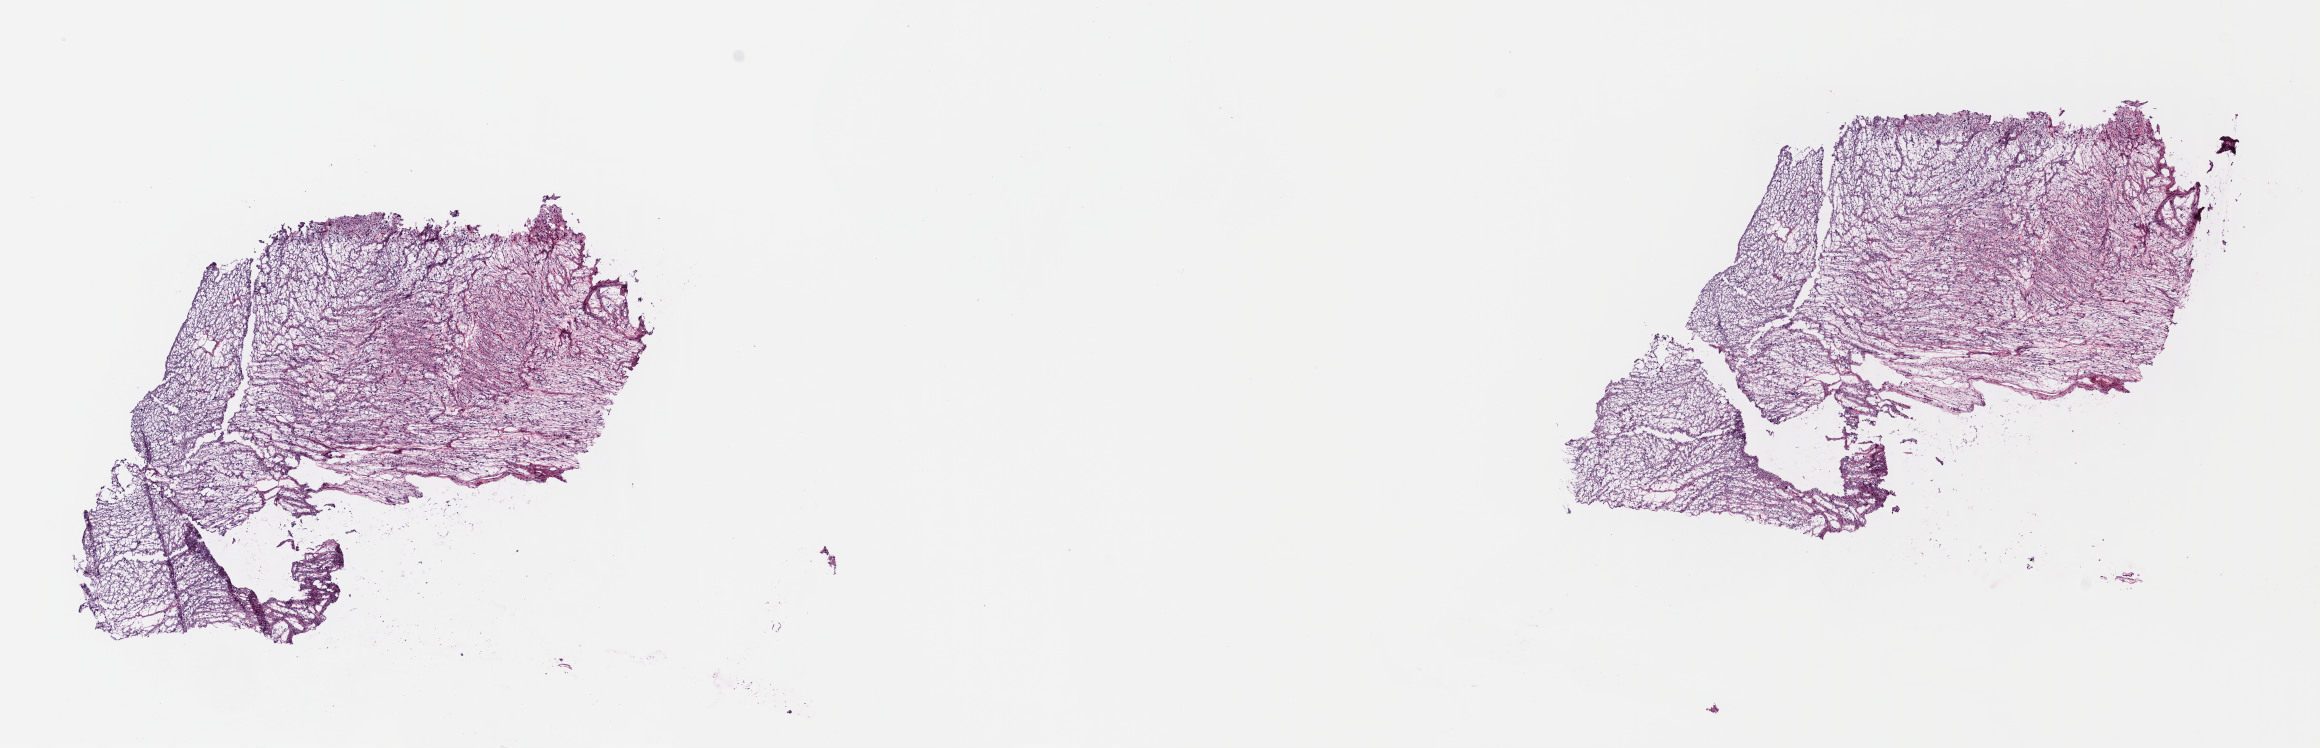
Whole-slide histology image, H&E-stained, whole scanned area (about 18.2 x 5.9 mm) shown as a low-resolution overview; frozen section from the top of the tissue portion; primary tumour sample from the connective, subcutaneous and other soft tissues. Male patient; age at initial diagnosis 59 years. Slide review estimates, as recorded: tumour cells 75%, tumour nuclei 75%, normal cells 0%, stromal cells 25%, necrosis 0%. Infiltration values recorded for this section: lymphocyte infiltration 3%, monocyte infiltration 2%, neutrophil infiltration 1%.
Pathologic diagnosis: Fibromyxosarcoma (connective, subcutaneous and other soft tissues of pelvis).